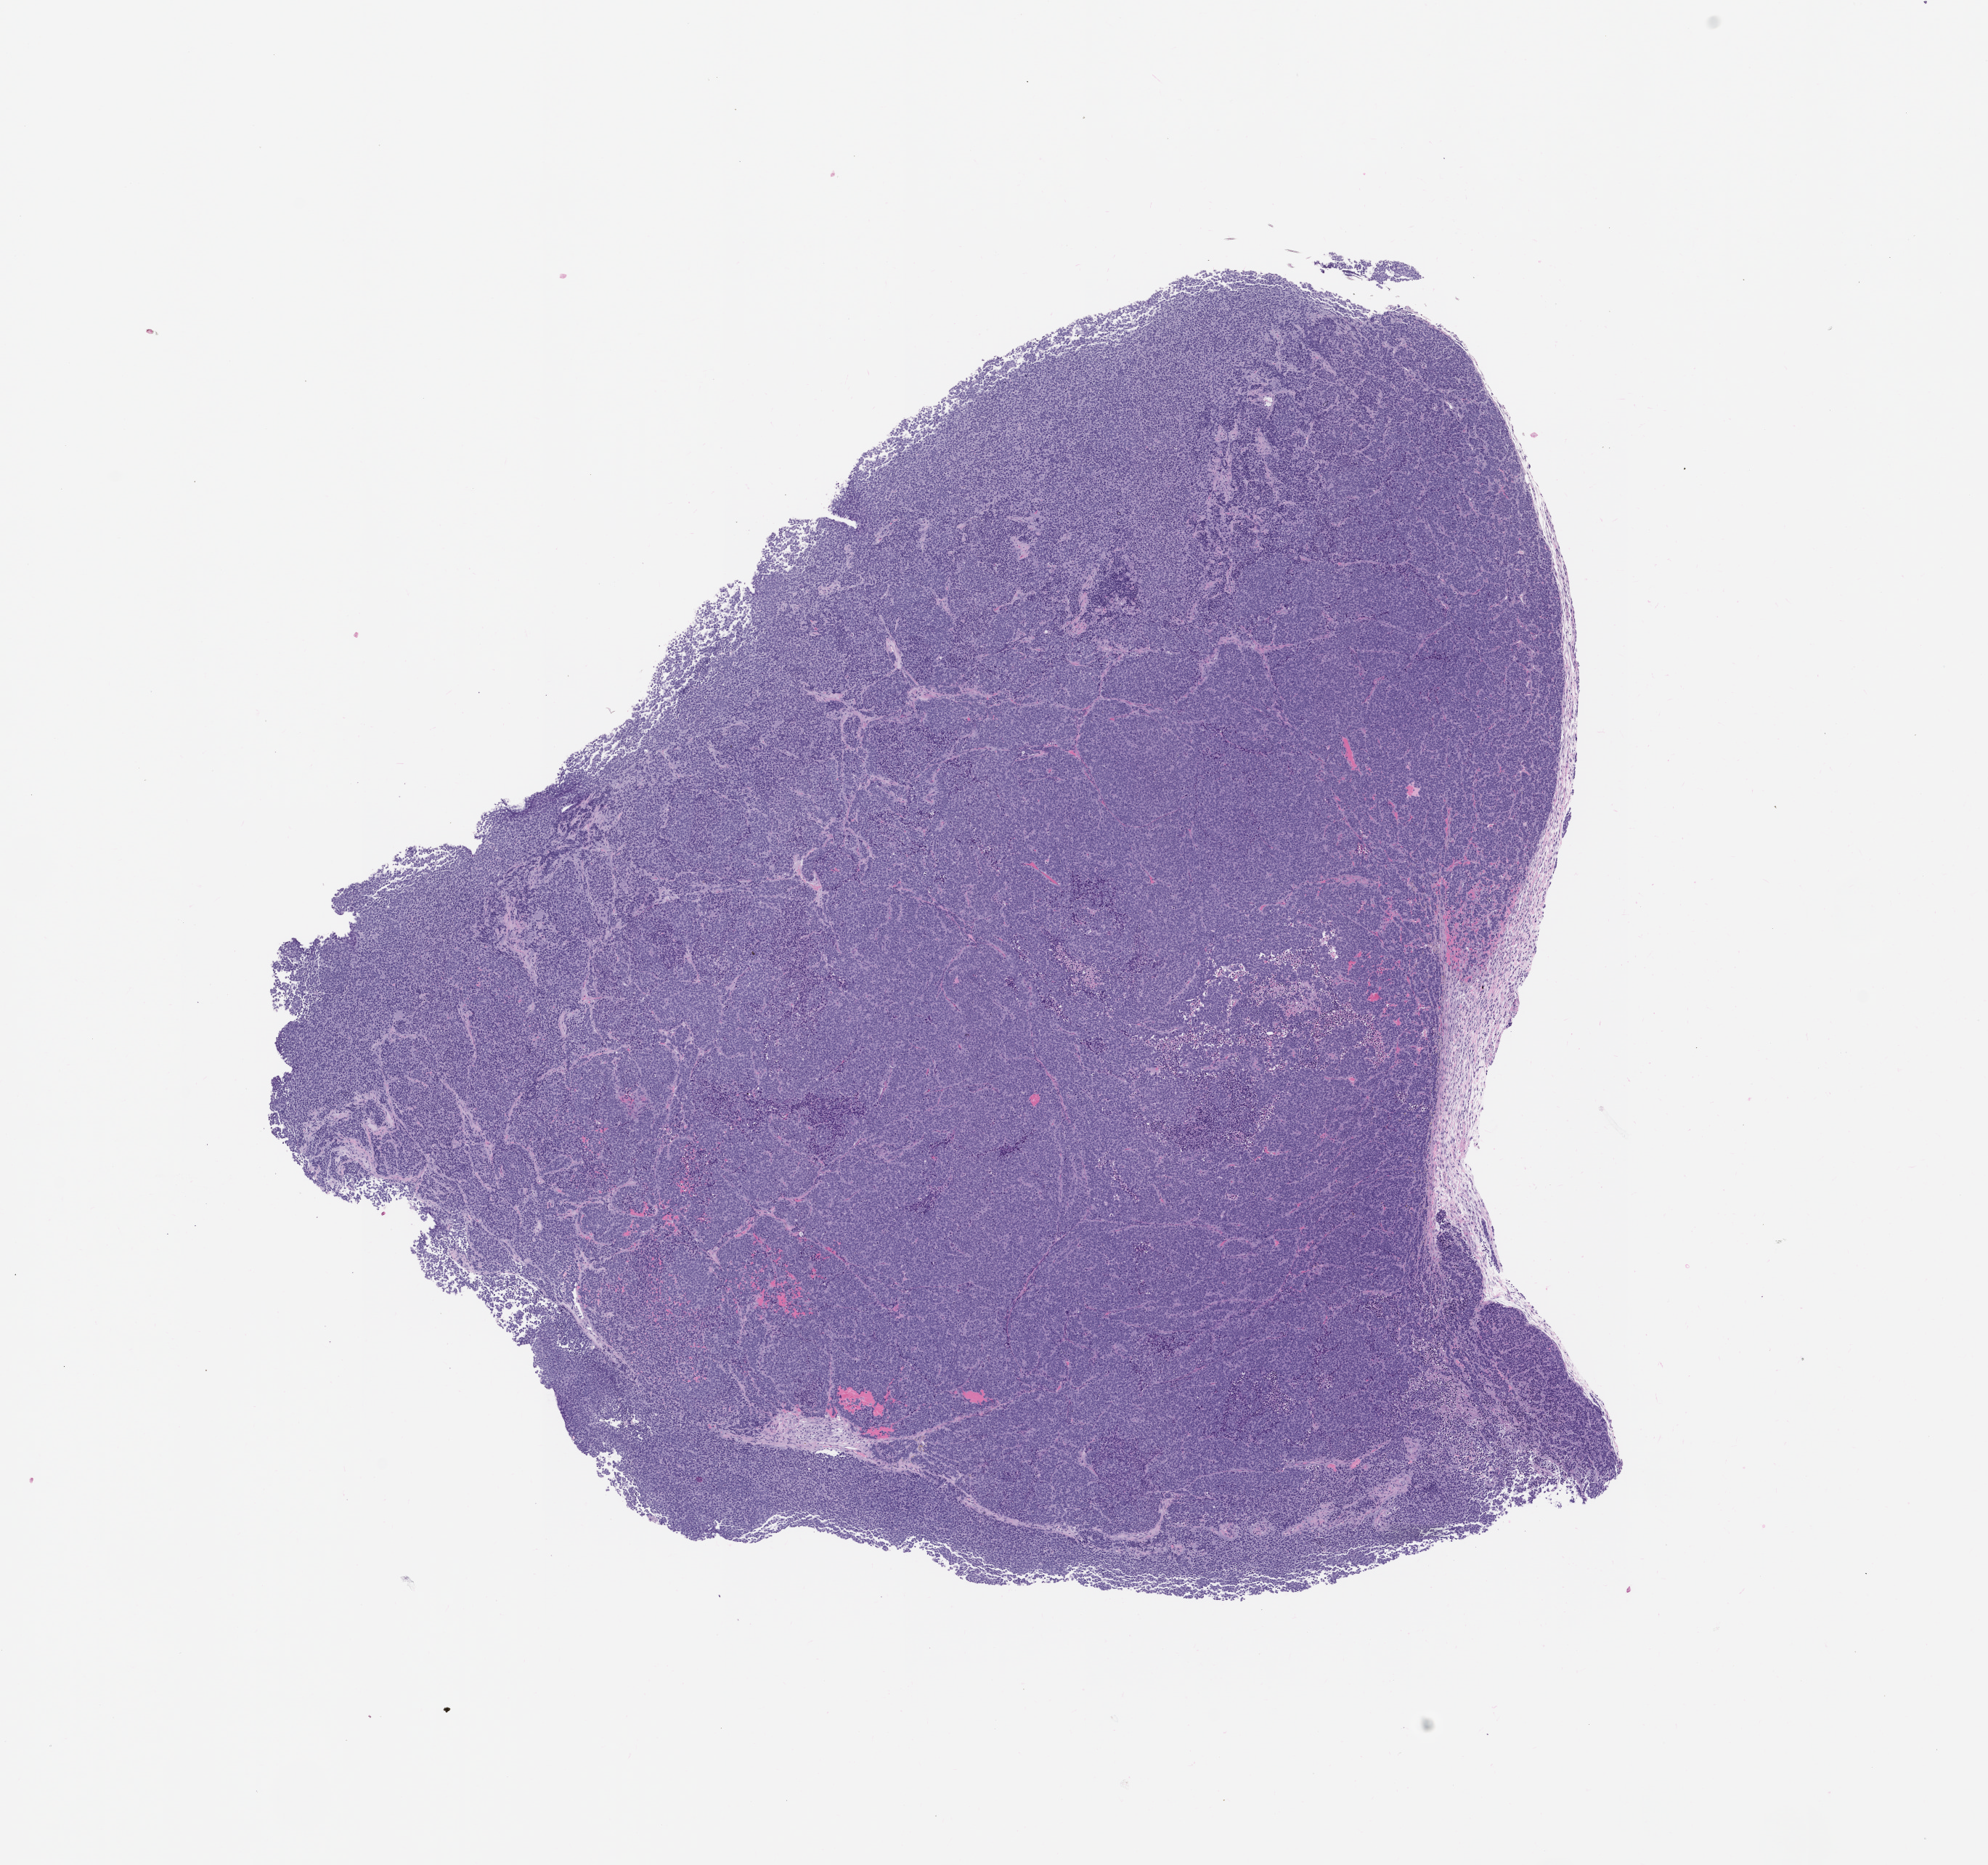
H&E whole-slide image of a patient-derived xenograft (PDX) tumor grown in a mouse, passage 0 — shown as a low-resolution overview of the whole scanned area (about 11.0 x 10.3 mm). FFPE section. Tumor site category: bladder.
Originating patient diagnosis: Bladder Small Cell Neuroendocrine Carcinoma.